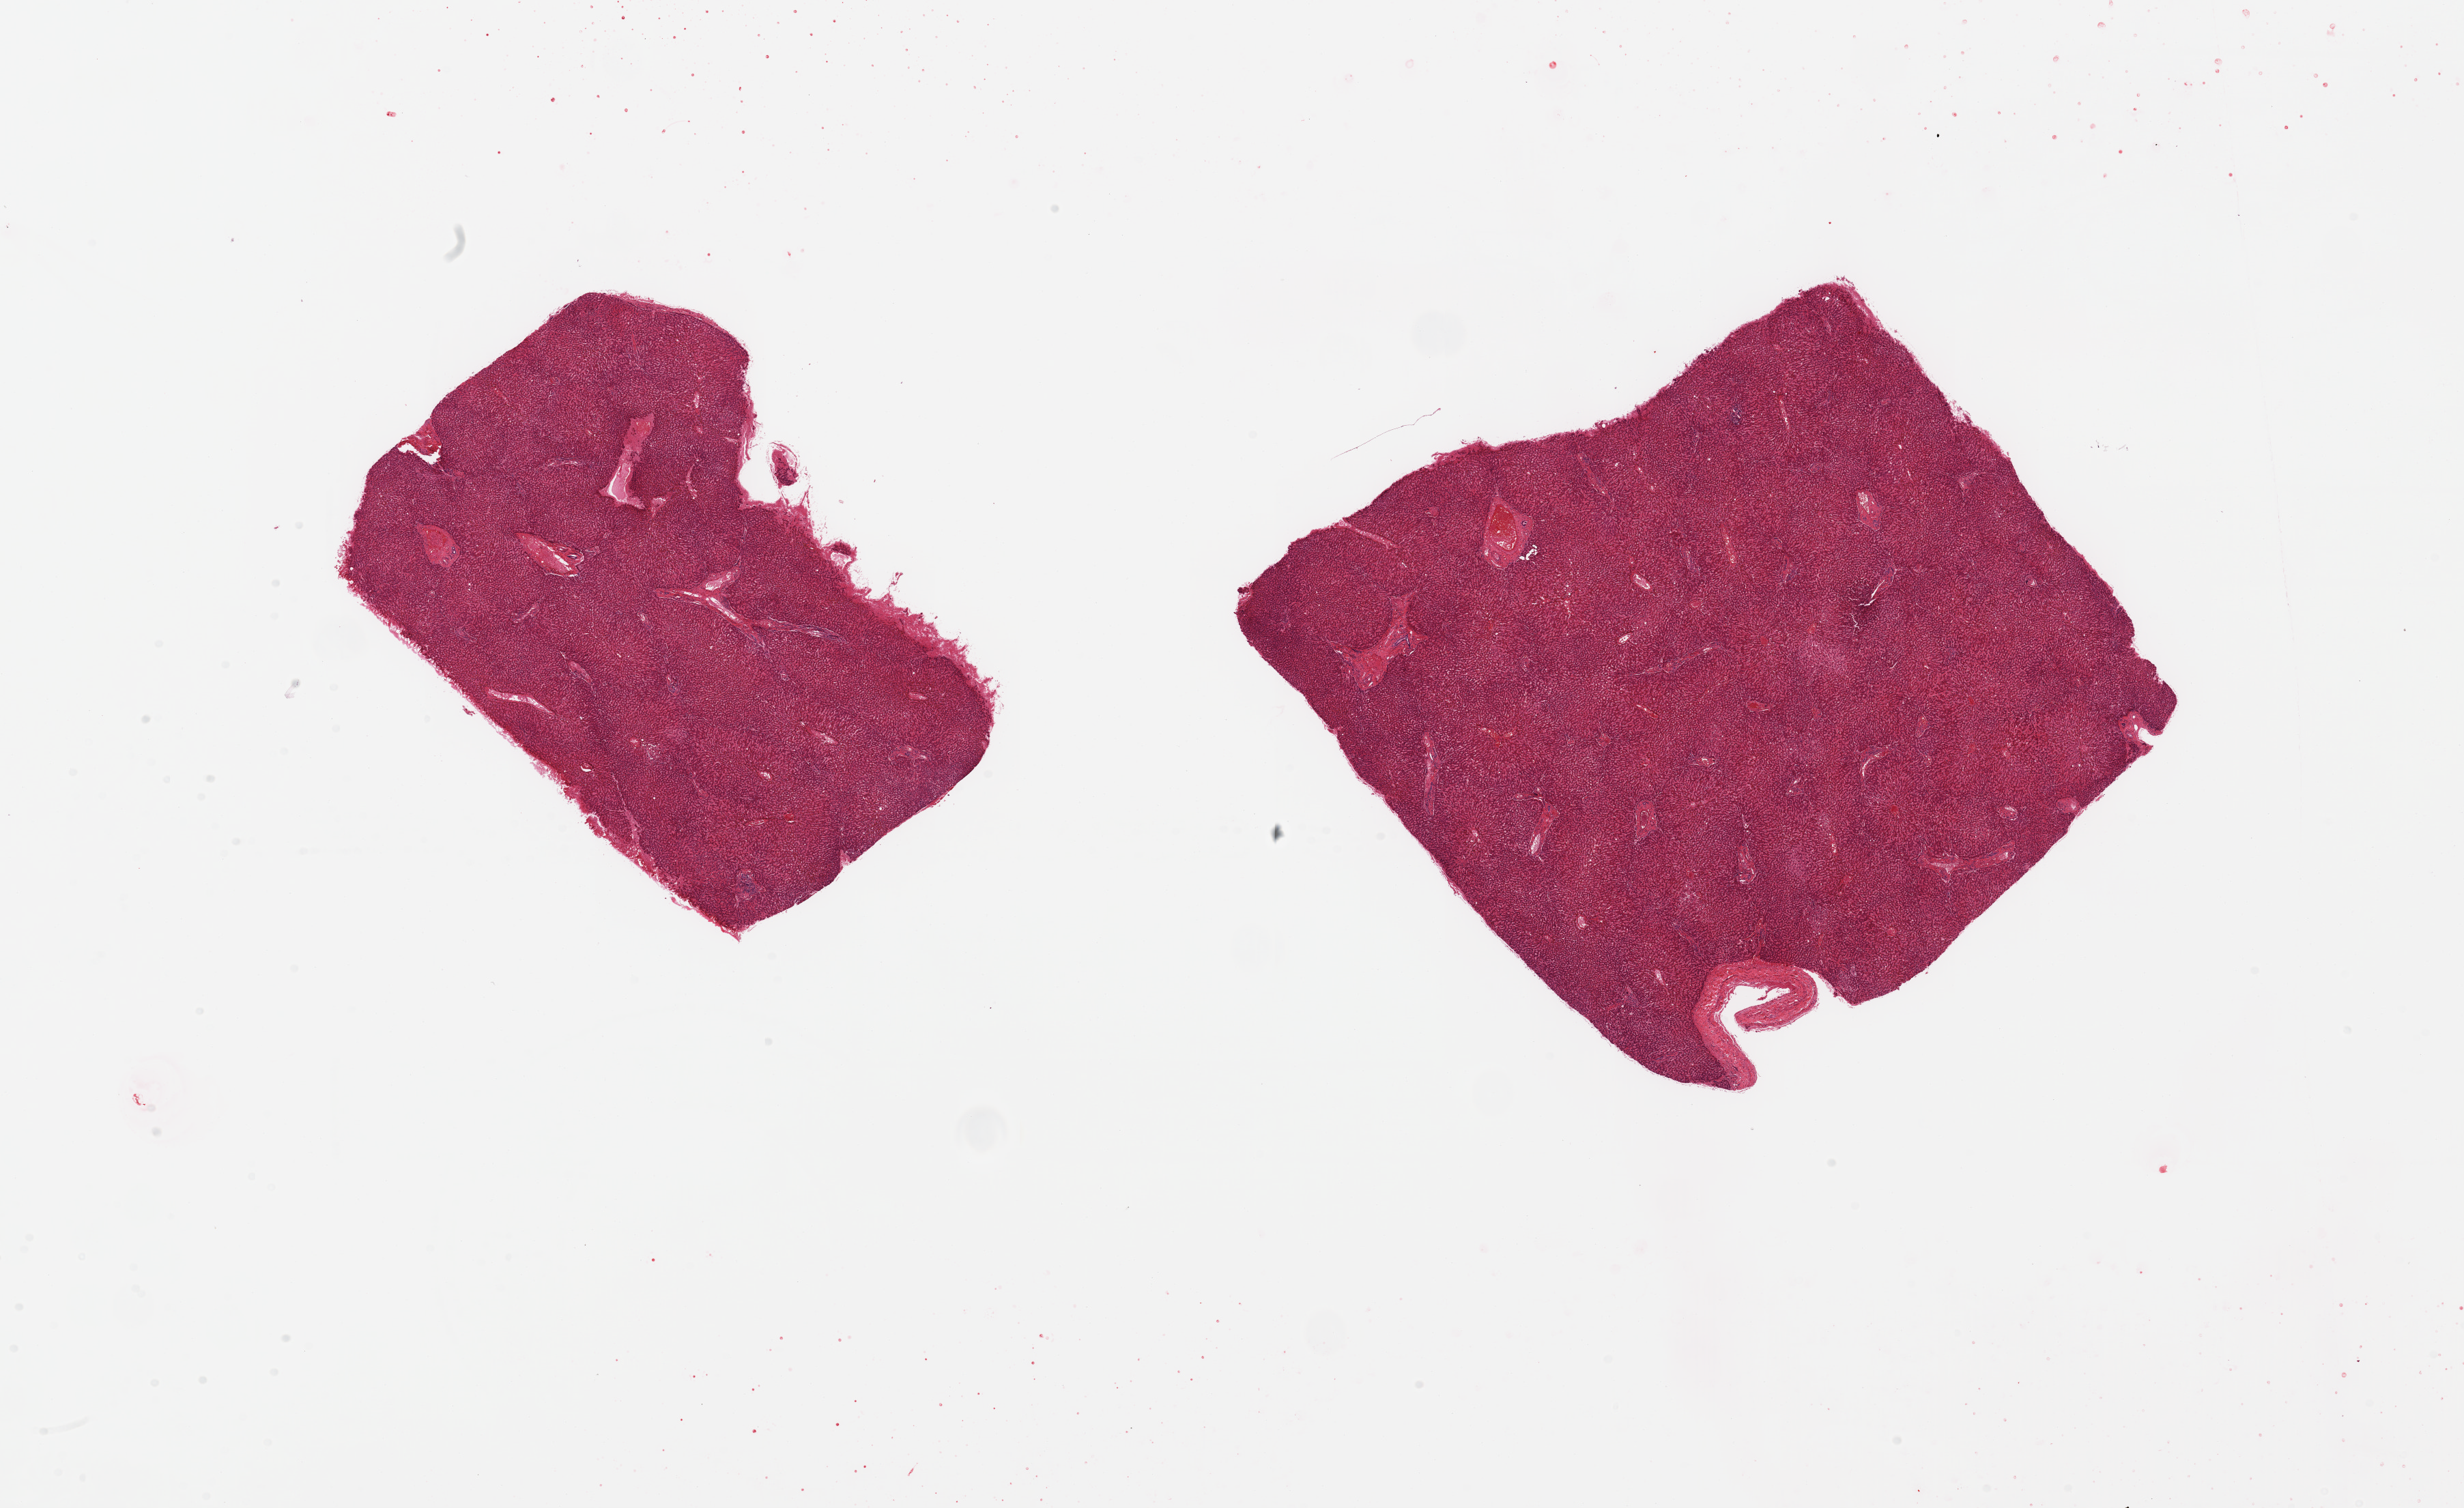
Whole-slide image, haematoxylin and eosin stain — whole scanned area (about 28.5 x 17.5 mm) shown as a low-resolution overview. PAXgene-fixed paraffin-embedded (PFPE) section. Target tissue: liver. Tissue donor sample. Donor sex: female.
• pathologist's review note for this sample: 2 pieces; <5% macrovesicular steatosis; no obvious iron accumulation [thalassemia history]